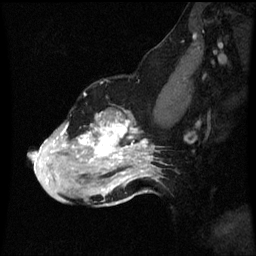
Breast MRI (dynamic contrast-enhanced), one sagittal slice; slice 39 of 60 in the series (ordered by position); dynamic contrast-enhanced series, image 2 of 3 at this slice position (ordered by acquisition); 1.5 T; TE 4.2 ms, TR 8.9 ms; 256 × 256 image matrix. Patient: female, 49 years. From the clinical record (not read from this slice): setting: breast cancer imaged before/during neoadjuvant chemotherapy; receptor status: HR-positive, HER2-negative.
Outlined on this slice (semi-automatic segmentation, software-assisted and operator-edited):
- analysis volume of interest (the breast-tissue region the enhancement analysis was run in; not a lesion): bounding box (x1, y1, x2, y2) in pixels: (28, 108, 159, 199)
- tumour enhancement mask (voxels above the 70 % enhancement threshold inside the analysis volume of interest): (32, 116, 151, 183)